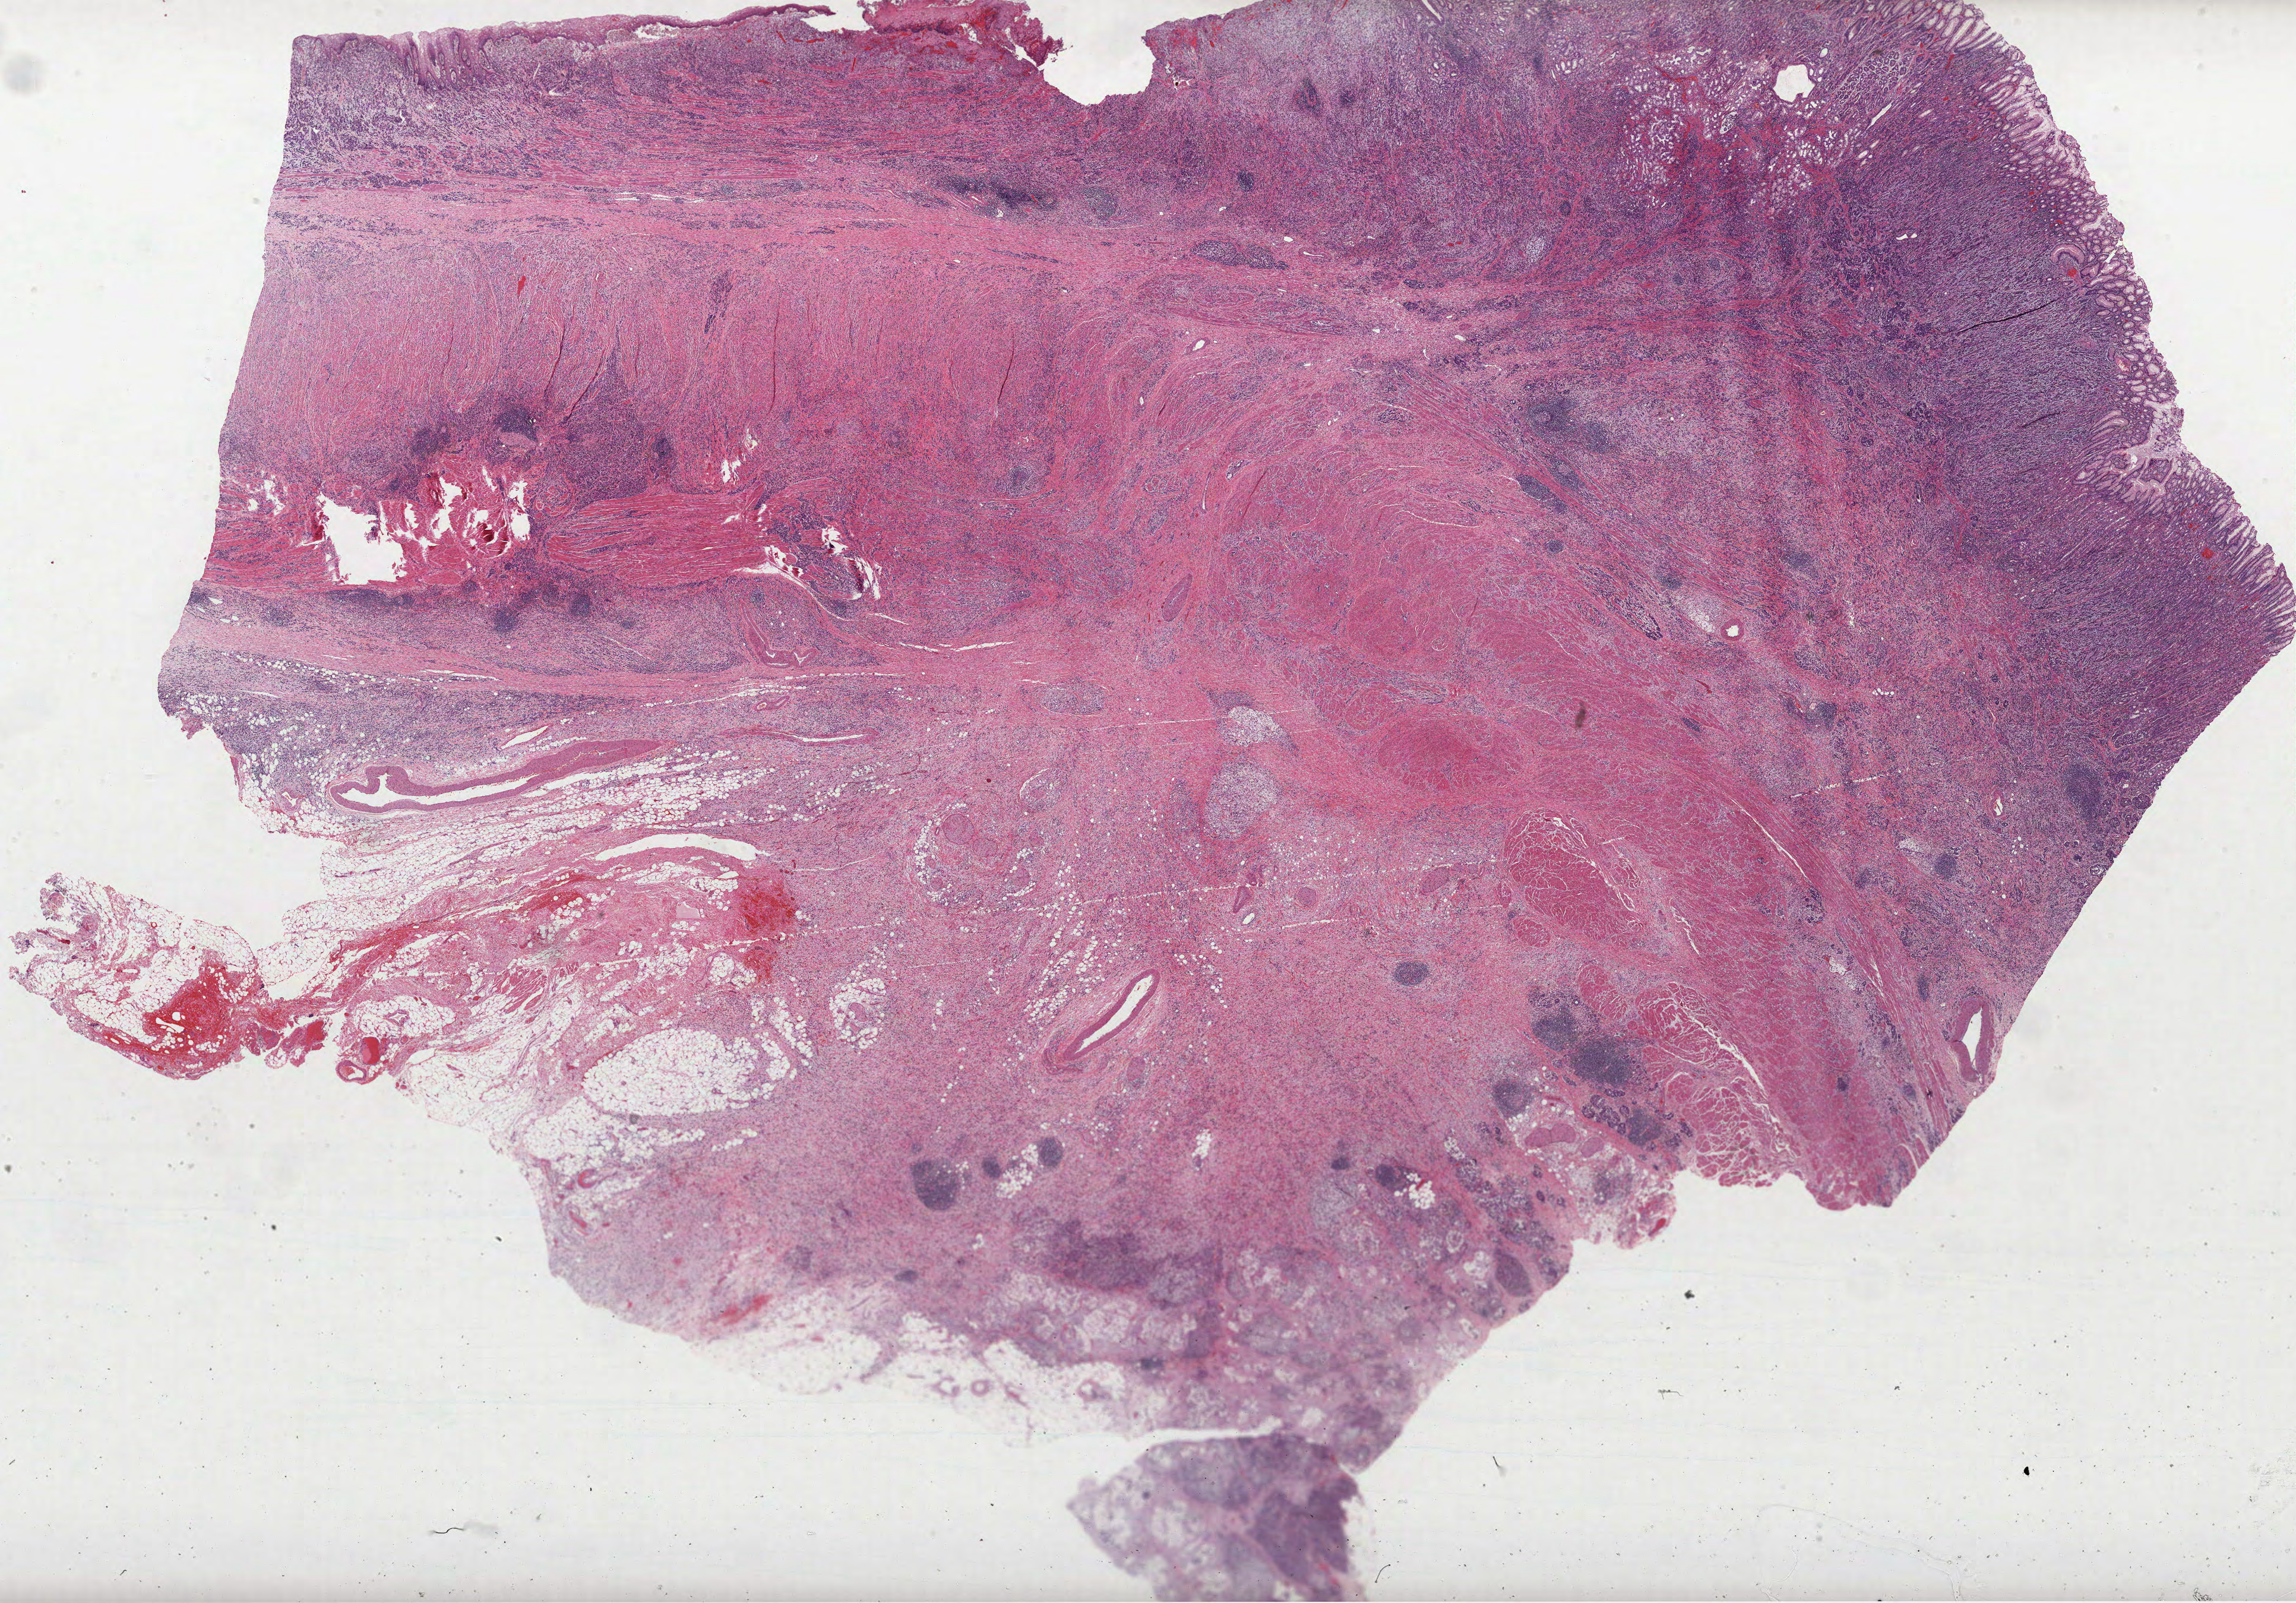
Digitized Hematoxylin and eosin (H&E) stained tissue section (whole slide) — low-resolution overview of the scanned area, about 31.2 x 21.8 mm. Formalin-fixed paraffin-embedded (FFPE) diagnostic section. Stomach, primary tumour sample. Male patient; age at initial diagnosis 59 years. Histologic grade: G3 (poorly differentiated).
Pathologic diagnosis: Carcinoma, diffuse type (cardia, NOS). Lymph nodes positive (case pathology): 21 of 24 examined.